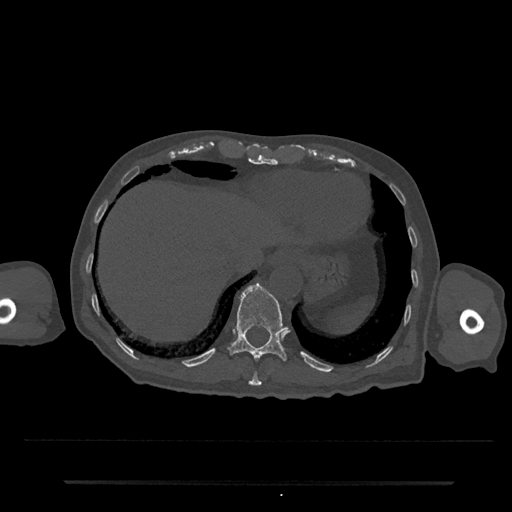
CT including the spine, one axial slice; position 260 of 797 along the scan axis; reconstruction kernel Br40s/3; bone window (W 1800 / L 400 HU); 0.5 mm slice thickness; 512 × 512 image matrix. Male patient, age 74 years. Case-level facts recorded for this patient, not image findings: primary cancer: prostate.
Annotated regions visible in this slice (semi-automatically segmented with operator editing):
- T10 vertebra: box from (x=248, y=372) to (x=262, y=386) px
- T11 vertebra: (x=227, y=283)–(x=289, y=361)